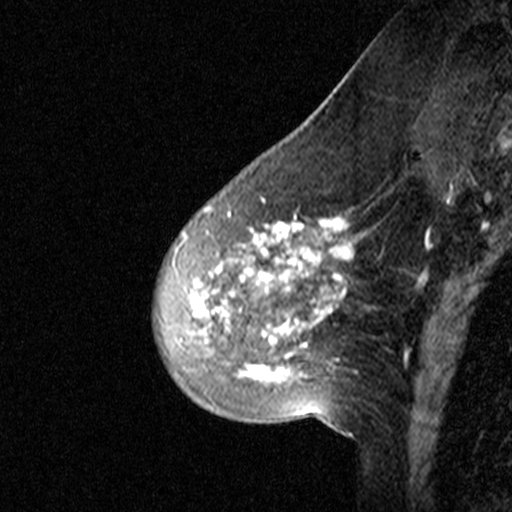
Breast MRI (dynamic contrast-enhanced), one sagittal slice. Dynamic contrast-enhanced study with each time point stored as its own series, time point 2 of 3 at this slice position (early post-contrast, ordered by acquisition time). 1.5 T. TE 4.5 ms, TR 11 ms. 512 × 512 image matrix. Patient: female, 46 years. Case-level facts recorded for this patient, not image findings: setting: breast cancer imaged before/during neoadjuvant chemotherapy; receptor status: HER2-positive.
Outlined on this slice (semi-automatically segmented with operator editing):
- analysis volume of interest (the breast-tissue region the enhancement analysis was run in; not a lesion): bounding box <152,172,359,393> (left, top, right, bottom; pixels)
- tumour enhancement mask (voxels above the 90 % enhancement threshold inside the analysis volume of interest): <191,198,347,379>